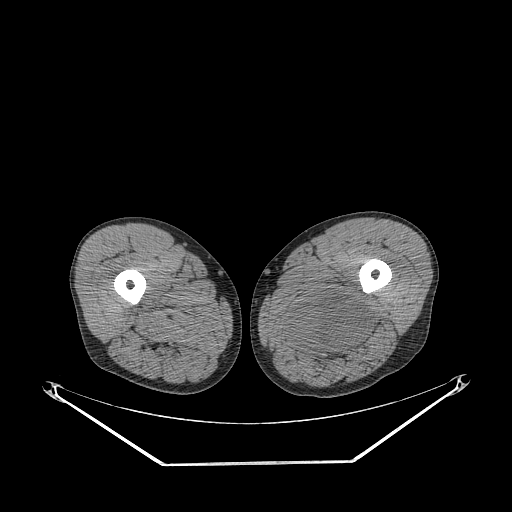
CT of an extremity soft-tissue mass (from a PET/CT study), one axial slice; position 253 of 267 along the scan axis; reconstruction kernel STANDARD; 140 kVp; soft-tissue window (W 400 / L 40 HU); 3.75 mm slice thickness; 512 × 512 image matrix, field of view 500 × 500 mm. Male patient. From the clinical record (not read from this slice): histological type: undifferentiated pleomorphic liposarcoma; grade: high; site of the primary tumour: left thigh.
Outlined on this slice (expert contour drawn on MRI and transferred to this co-registered scan by the dataset authors):
- gross tumour volume including surrounding oedema: box from (x=281, y=290) to (x=371, y=359) px
- gross tumour volume (mass): (x=290, y=292)–(x=369, y=352)